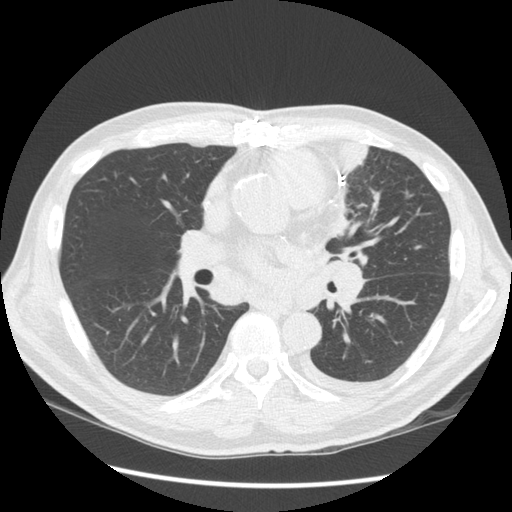
Low-dose screening chest CT, one axial slice. 120 kVp. Lung window (W 1500 / L -600 HU). 2.5 mm slice thickness. 512 × 512 image matrix, field of view 360 × 360 mm.
Annotated regions visible in this slice (expert manual segmentation):
- lesion 1 (tumor, upper lobe of left lung): box from (x=331, y=140) to (x=368, y=237) px